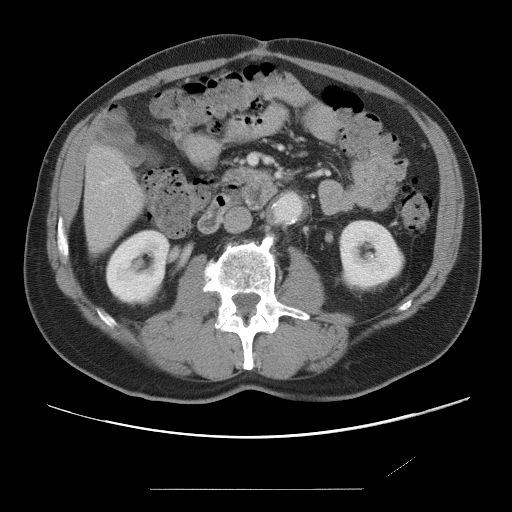
Contrast-enhanced abdominal CT, one axial slice; slice 17 of 87 in the series (ordered by position); 120 kVp; soft-tissue window (W 400 / L 40 HU); 5 mm slice thickness; 512 × 512 image matrix, field of view 406 × 406 mm. Male patient, age 74 years. Case-level facts recorded for this patient, not image findings: diagnosis: colorectal cancer liver metastases, imaged before liver resection; multiple liver metastases: yes; largest metastasis: 1.1 cm; chemotherapy before resection: yes.
Structures marked on this image (expert manual segmentation):
- hepatic veins: box from (x=102, y=179) to (x=112, y=185) px
- liver: (x=85, y=148)–(x=142, y=252)
- planned liver remnant (the part of the liver to remain after resection): (x=85, y=148)–(x=142, y=252)